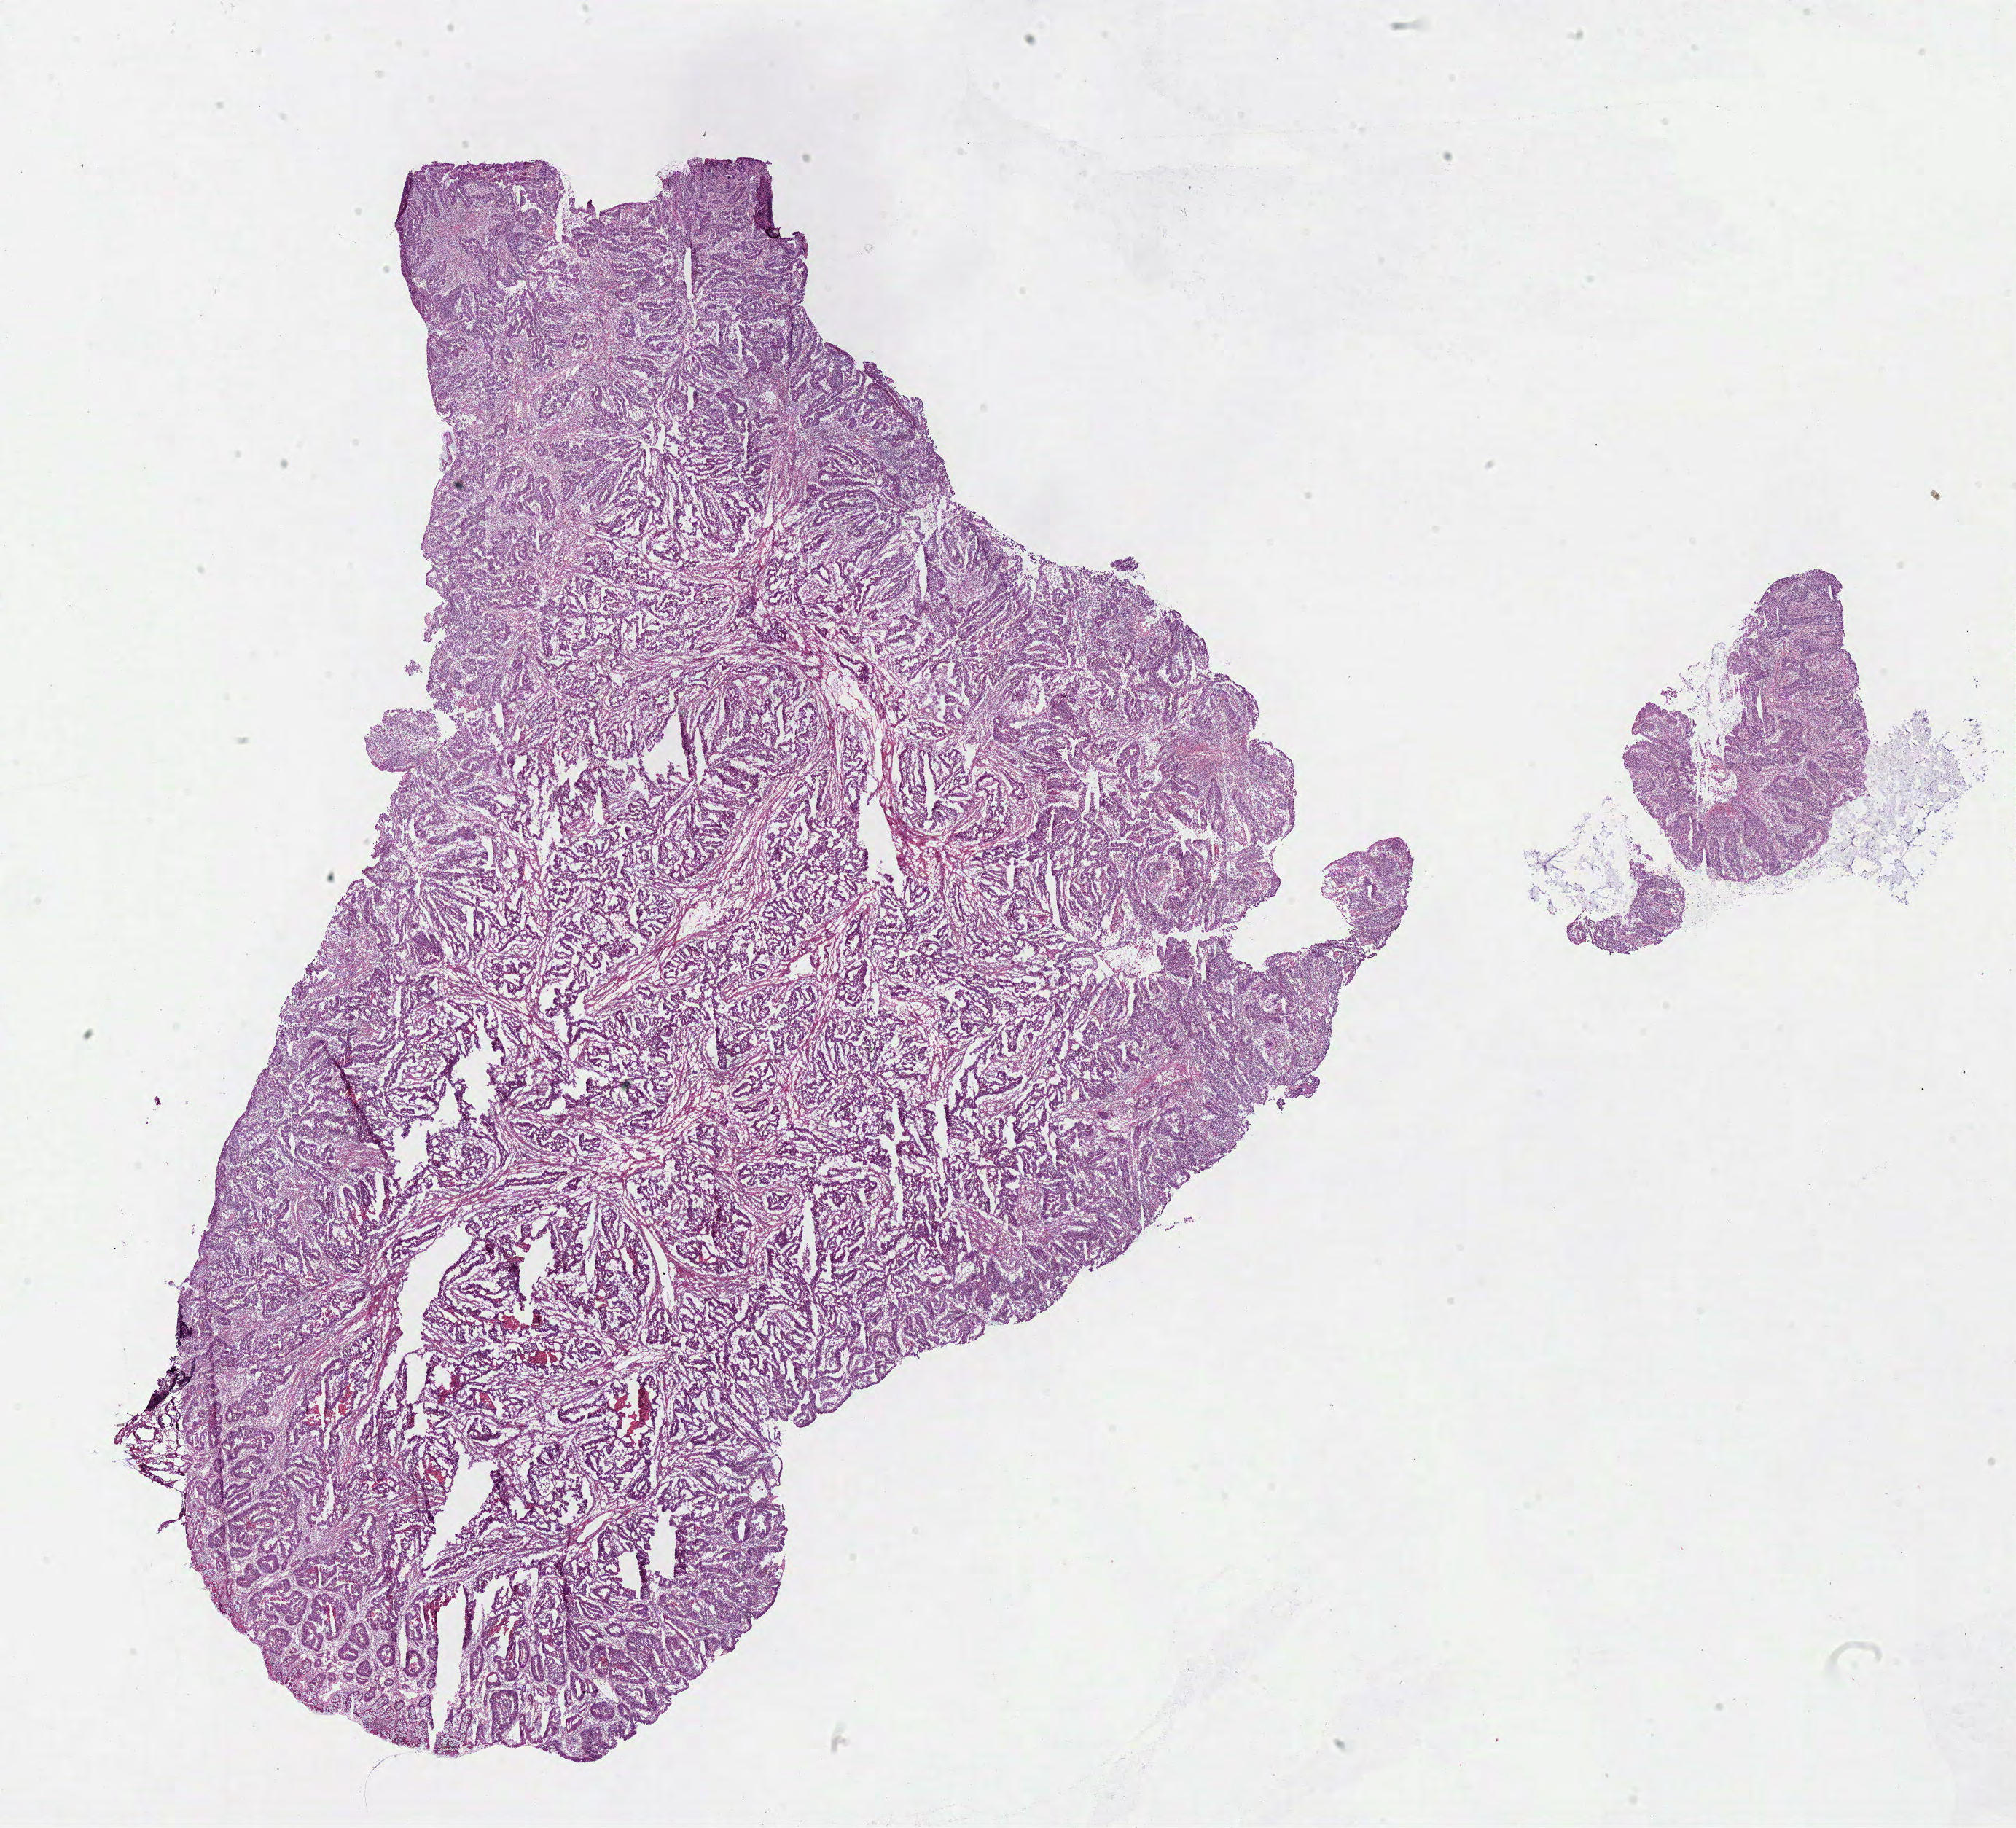
Digitized H&E-stained tissue section (whole slide) — whole scanned area (about 21.8 x 19.8 mm, from a 40x scan) shown as a low-resolution overview. Frozen section from the bottom of the tissue portion. Primary tumour sample from the rectum. Female, age 31 years at initial diagnosis. Pathologist review of this section (percent, as recorded): tumour cells 85%, tumour nuclei 75%, normal cells 0%, stromal cells 10%, necrosis 5%. Inflammatory infiltration, as recorded: lymphocyte infiltration 20%, monocyte infiltration 0%, neutrophil infiltration 0%.
Histologic diagnosis: Adenocarcinoma, NOS (rectosigmoid junction). AJCC pathologic stage: IIIA. TNM: T2 N1b M0. Lymph nodes positive (case pathology): 3 of 31 examined.